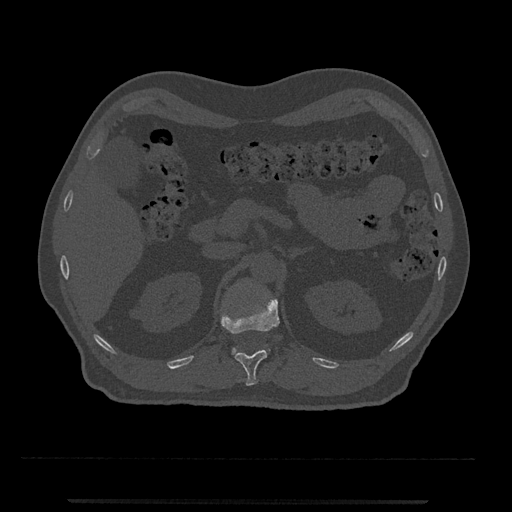
CT including the spine, one axial slice. Position 379 of 797 along the scan axis. Reconstruction kernel Br40s/3. Bone window (W 1800 / L 400 HU). 512 × 512 image matrix, field of view 419 × 419 mm. Patient: male, 63 years. Case-level facts recorded for this patient, not image findings: primary cancer: prostate.
Outlined on this slice (semi-automatically segmented with operator editing):
- L1 vertebra: bounding box [x1, y1, x2, y2] px = [231, 348, 267, 354]
- T12 vertebra: [221, 296, 280, 386]